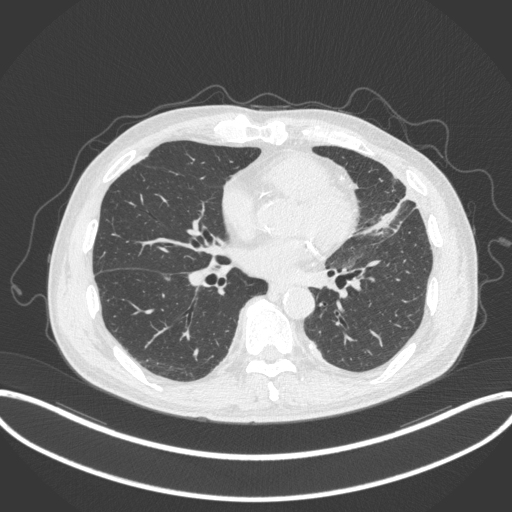
Chest CT, one axial slice. Slice 145 of 382 in the series (ordered by position). 120 kVp. Lung window (W 1500 / L -600 HU). 512 × 512 image matrix. Patient: male, 64 years. Case-level facts recorded for this patient, not image findings: clinical TNM (as recorded): T4 N1 M0; histopathological grade: G3.
Annotated regions visible in this slice (bounding box drawn by a radiologist):
- lung tumour (recorded histology: adenocarcinoma): bounding box <355,194,412,241> (left, top, right, bottom; pixels)